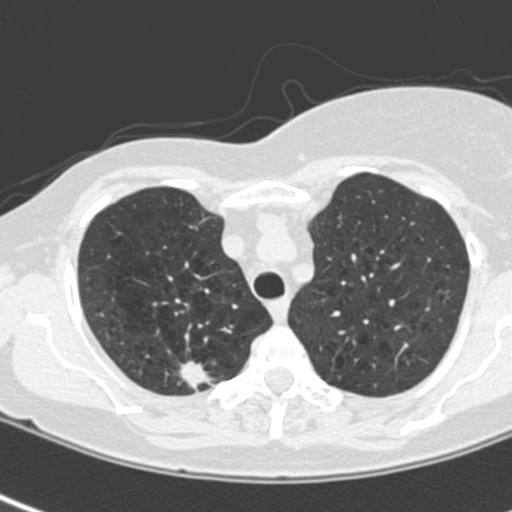
Low-dose screening chest CT, one axial slice. Position 177 of 214 along the scan axis. 120 kVp. Lung window (W 1500 / L -600 HU). 512 × 512 image matrix.
Annotated regions visible in this slice (manually delineated by an expert):
- lesion 1 (tumor, upper lobe of right lung): bounding box (x1, y1, x2, y2) in pixels: (179, 361, 207, 390)